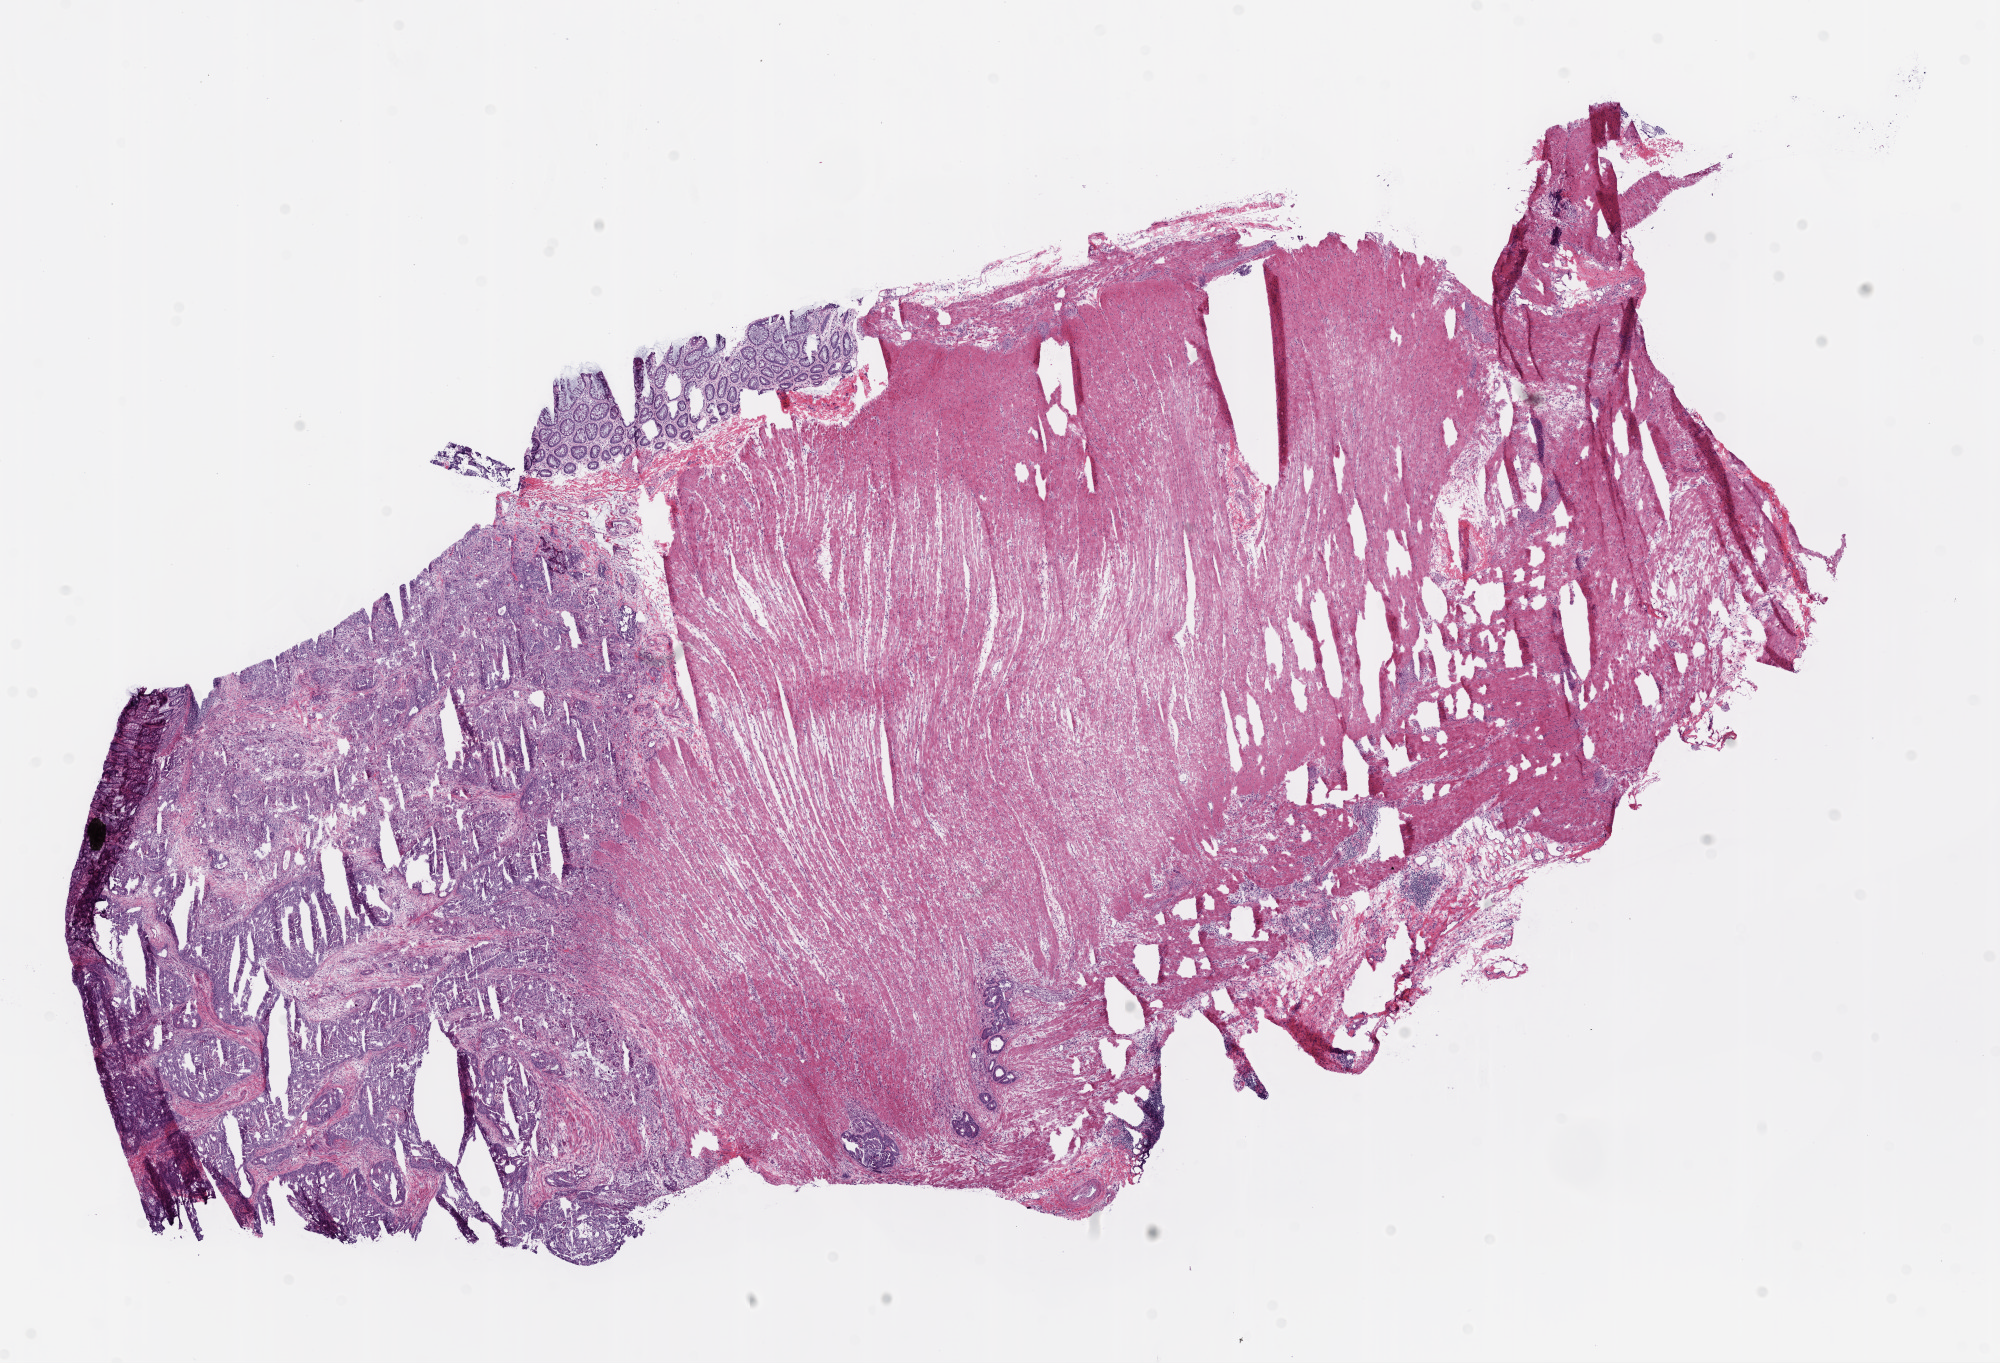
Whole-slide histology image, H&E — shown as a low-resolution overview of the whole scanned area (about 16.0 x 10.9 mm, slide scanned at 20x), frozen section from the bottom of the tissue portion, primary tumour sample from the colon. Female, age 48 years at initial diagnosis. Pathologist review of this section (percent, as recorded): tumour cells 34%, tumour nuclei 70%, normal cells 60%, stromal cells 5%, necrosis 1%.
Histologic diagnosis: Adenocarcinoma, NOS. Lymph nodes positive (case pathology): 0 of 29 examined. TNM: T3 N0 M0. AJCC pathologic stage: IIA.